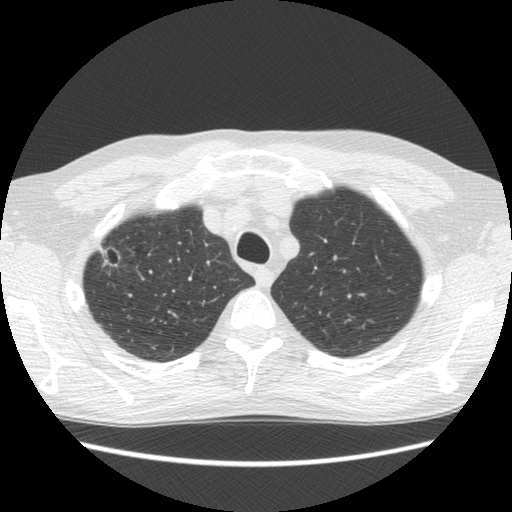
Low-dose screening chest CT, one axial slice; position 101 of 125 along the scan axis; reconstruction kernel STANDARD; 120 kVp; lung window (W 1500 / L -600 HU); 2.5 mm slice thickness; 512 × 512 image matrix, field of view 350 × 350 mm.
Outlined on this slice (outlined manually by an expert reader):
- lesion 1 (tumor, upper lobe of right lung): bounding box (x1, y1, x2, y2) in pixels: (101, 249, 111, 265)